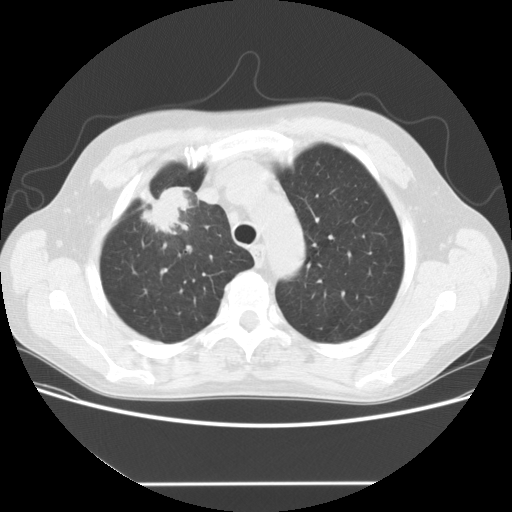
Chest CT (low-dose screening protocol), one axial image. First (baseline) screen. Lung window (W 1500 / L -600 HU). 2.5 mm slice thickness. Standard (soft-tissue) reconstruction kernel (STANDARD). 120 kVp. Slice 32 of 153 in the series. 512 × 512 image matrix, field of view 360 × 360 mm. Male, age 56 years at enrolment. Current smoker at enrolment.
- Lesion marked by an expert reader, bounding box (x1, y1, x2, y2) in pixels: (128, 175, 209, 242).
- The screening reader recorded 2 non-calcified nodules or masses ≥4 mm on this exam (right upper lobe, right middle lobe); which of them this box marks is not recorded.
- Official screen result: positive, change unspecified: nodule(s) >= 4 mm or enlarging nodule(s), mass(es), or other non-specific abnormalities suspicious for lung cancer.
- Lung cancer was diagnosed 120 days after this screen: adenocarcinoma, NOS, right upper lobe, stage IIIA (AJCC 6th edition), 34 mm at pathology.